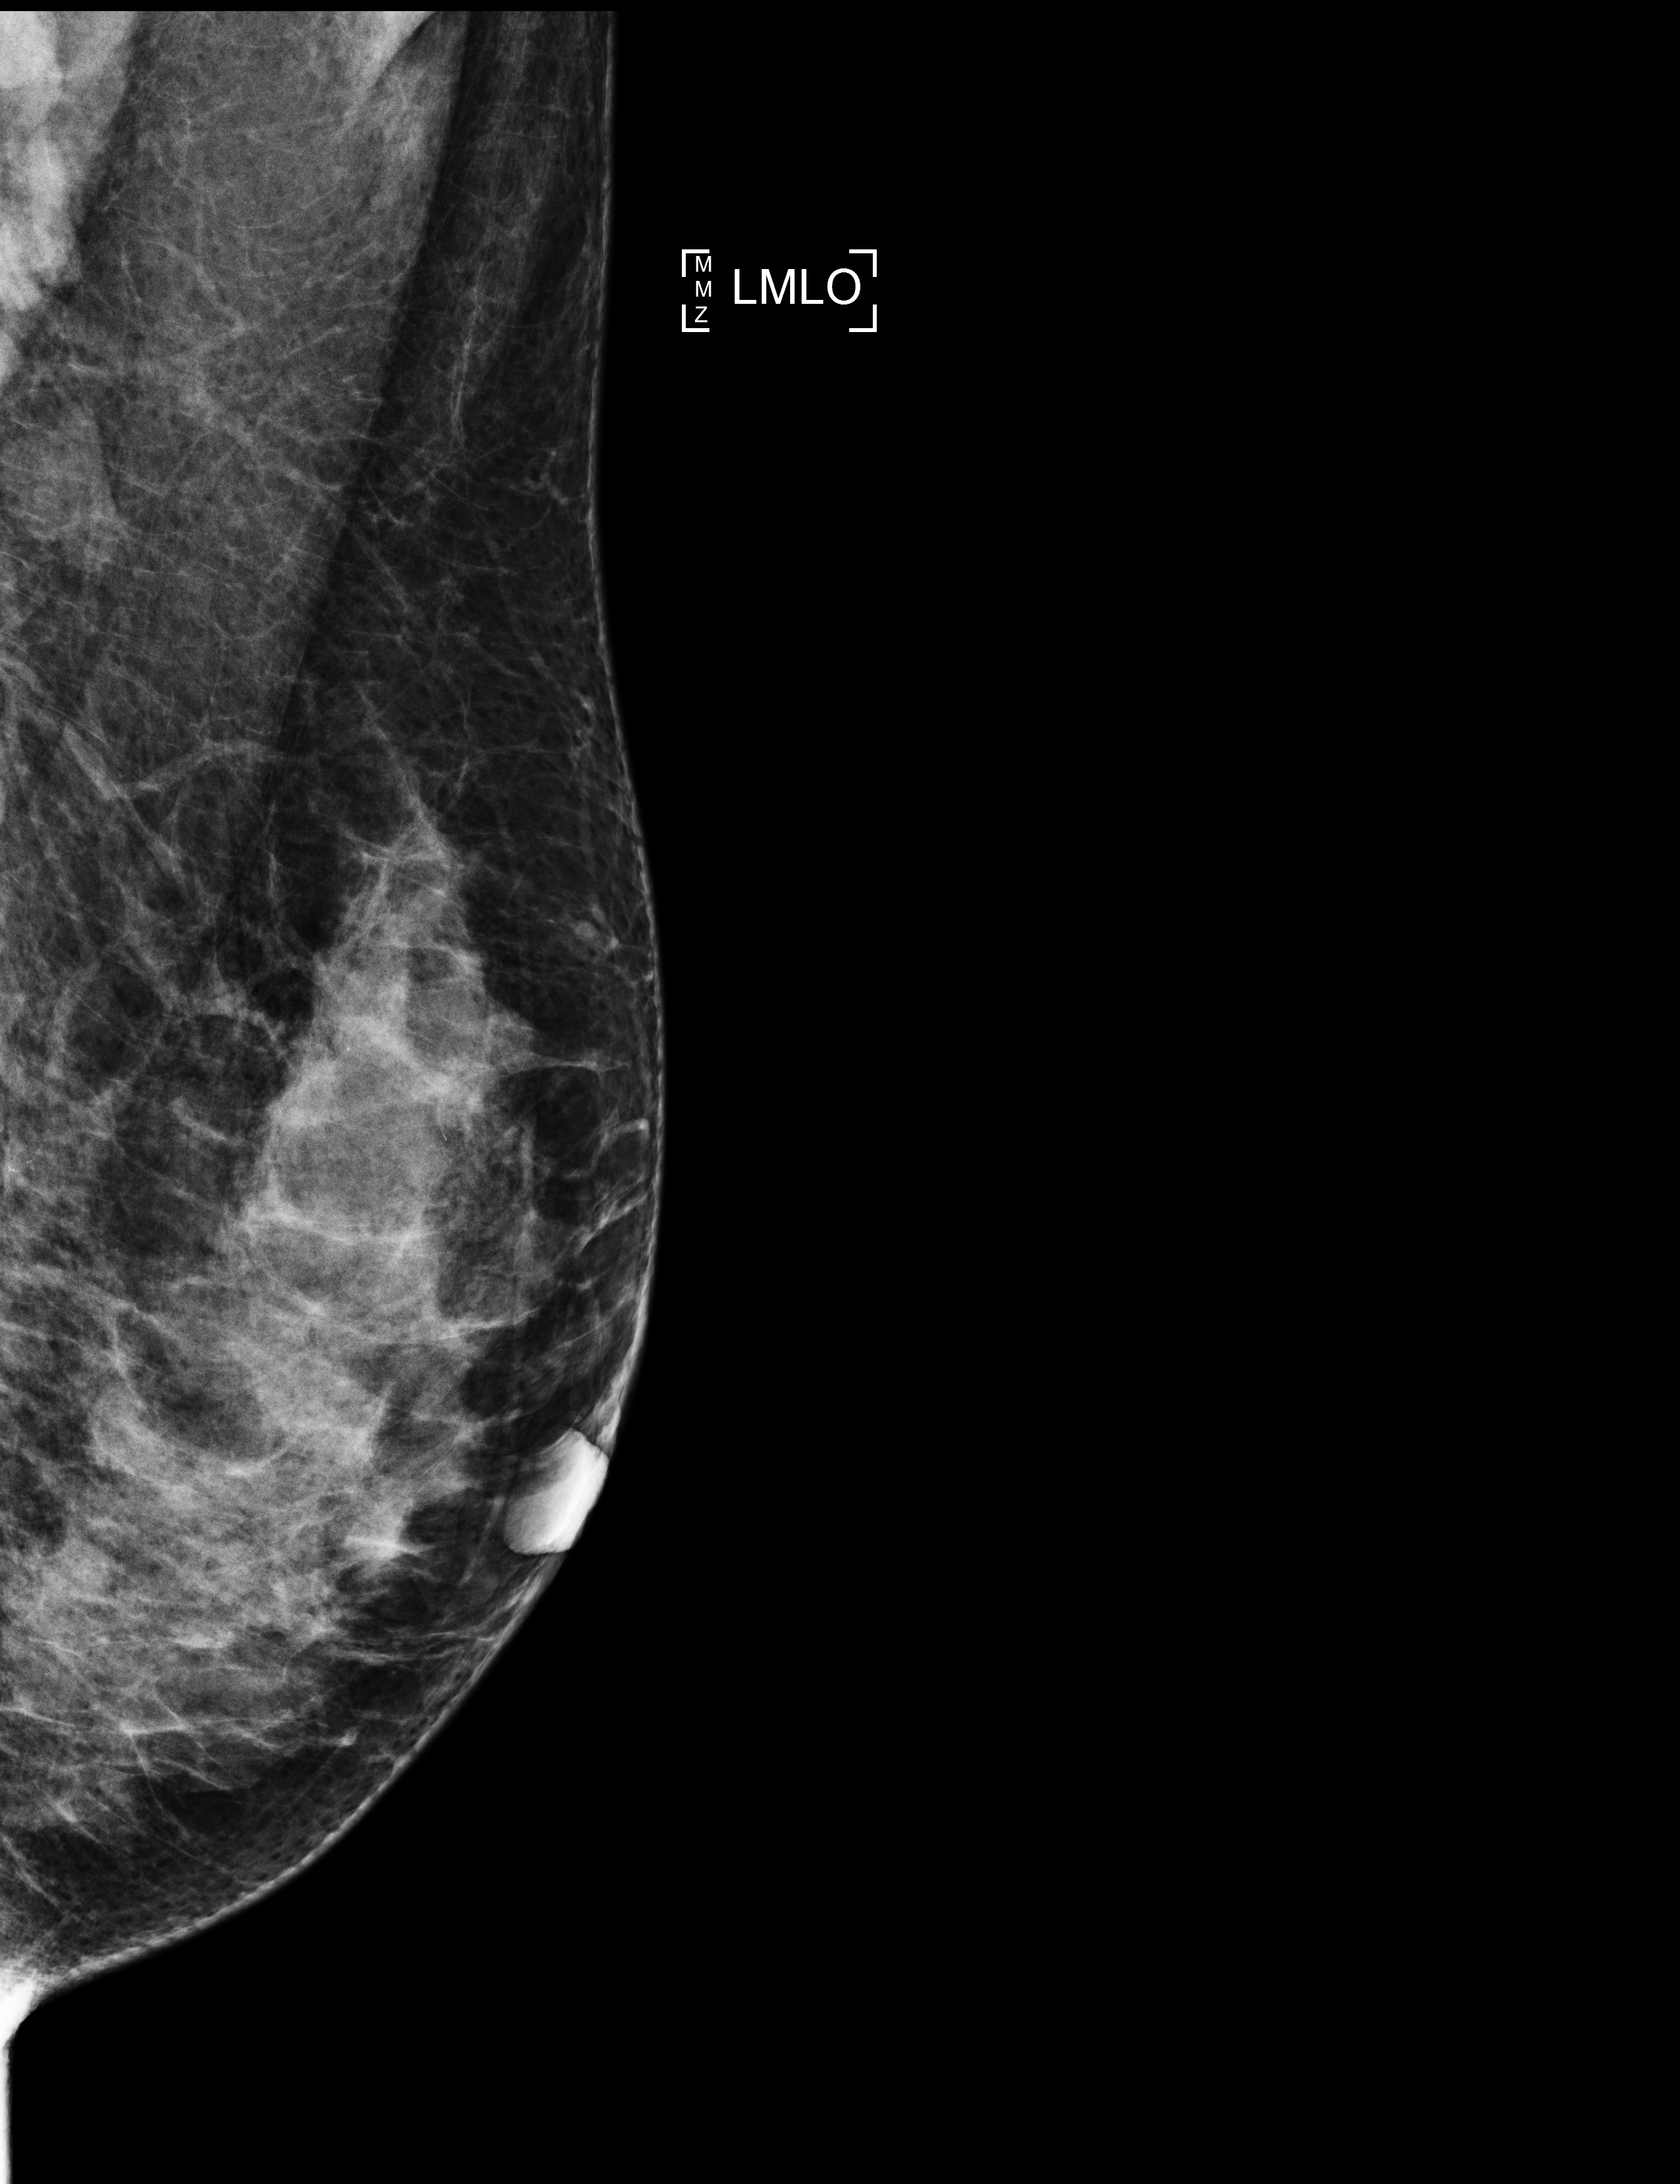
Full-field digital mammogram (FFDM), left breast, MLO view, screening examination, compressed breast thickness 50 mm, system: Selenia Dimensions. Female patient, age 47 years.
- breast density at the screening exam (both breasts): heterogeneously dense (BI-RADS density category c)
- final BI-RADS assessment for this screening round (tomosynthesis exam, both breasts): category 1
- recall: no recall after this screen